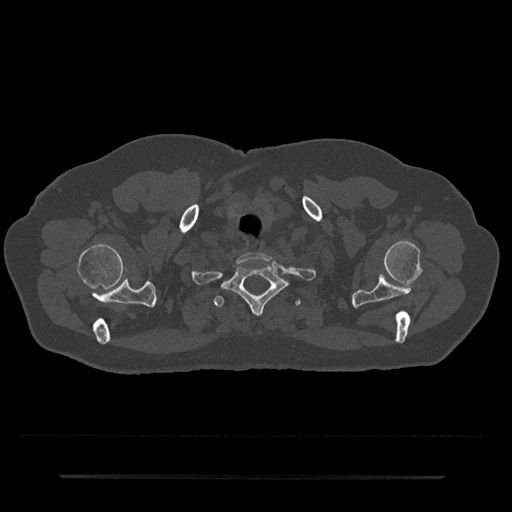
CT including the spine, one axial slice. Position 639 of 797 along the scan axis. Bone window (W 1800 / L 400 HU). 0.5 mm slice thickness. 512 × 512 image matrix. Patient: male, 69 years. From the clinical record (not read from this slice): primary cancer: prostate.
Annotated regions visible in this slice (semi-automatically segmented with operator editing):
- T1 vertebra: bounding box [x1, y1, x2, y2] px = [221, 263, 287, 314]
- T2 vertebra: [214, 287, 300, 308]